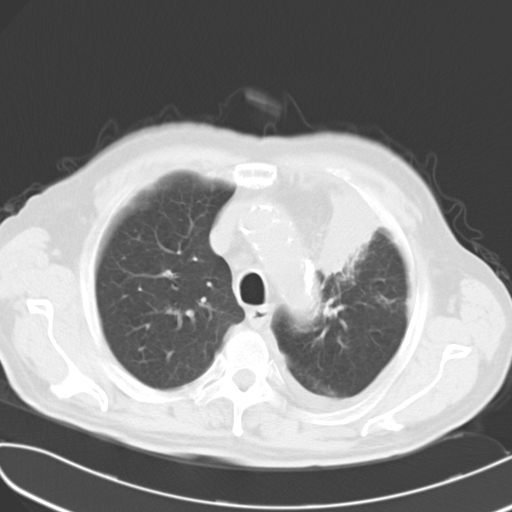
Chest CT, one axial slice; position 21 of 27 along the scan axis; 120 kVp; lung window (W 1500 / L -600 HU); 10 mm slice thickness; 512 × 512 image matrix. Male patient, age 70 years. From the clinical record (not read from this slice): clinical TNM (as recorded): T2 N1 M3; histopathological grade: G3.
Outlined on this slice (bounding box drawn by a radiologist):
- lung tumour (recorded histology: small cell carcinoma): bounding box [x1, y1, x2, y2] px = [316, 175, 395, 290]